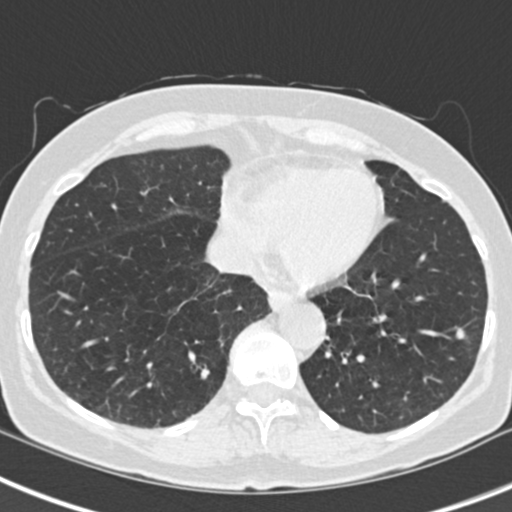
Low-dose screening chest CT, one axial slice. Slice 75 of 229 in the series (ordered by position). Reconstruction kernel B30f. Lung window (W 1500 / L -600 HU). 512 × 512 image matrix, field of view 296 × 296 mm.
Annotated regions visible in this slice (manually delineated by an expert):
- lesion 1 (tumor): bounding box <457,327,465,339> (left, top, right, bottom; pixels)